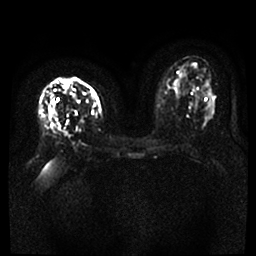
Breast MRI, one axial slice. Position 17 of 46 along the scan axis. Diffusion-weighted series; image 2 of 4 stored at this slice position (different b-values; order by instance number). 1.5 T. 4 mm slice thickness. 256 × 256 image matrix, field of view 360 × 360 mm. Female patient.
Structures marked on this image (manually delineated by an expert):
- tumour on diffusion-weighted imaging: bounding box (x1, y1, x2, y2) in pixels: (51, 100, 54, 113)